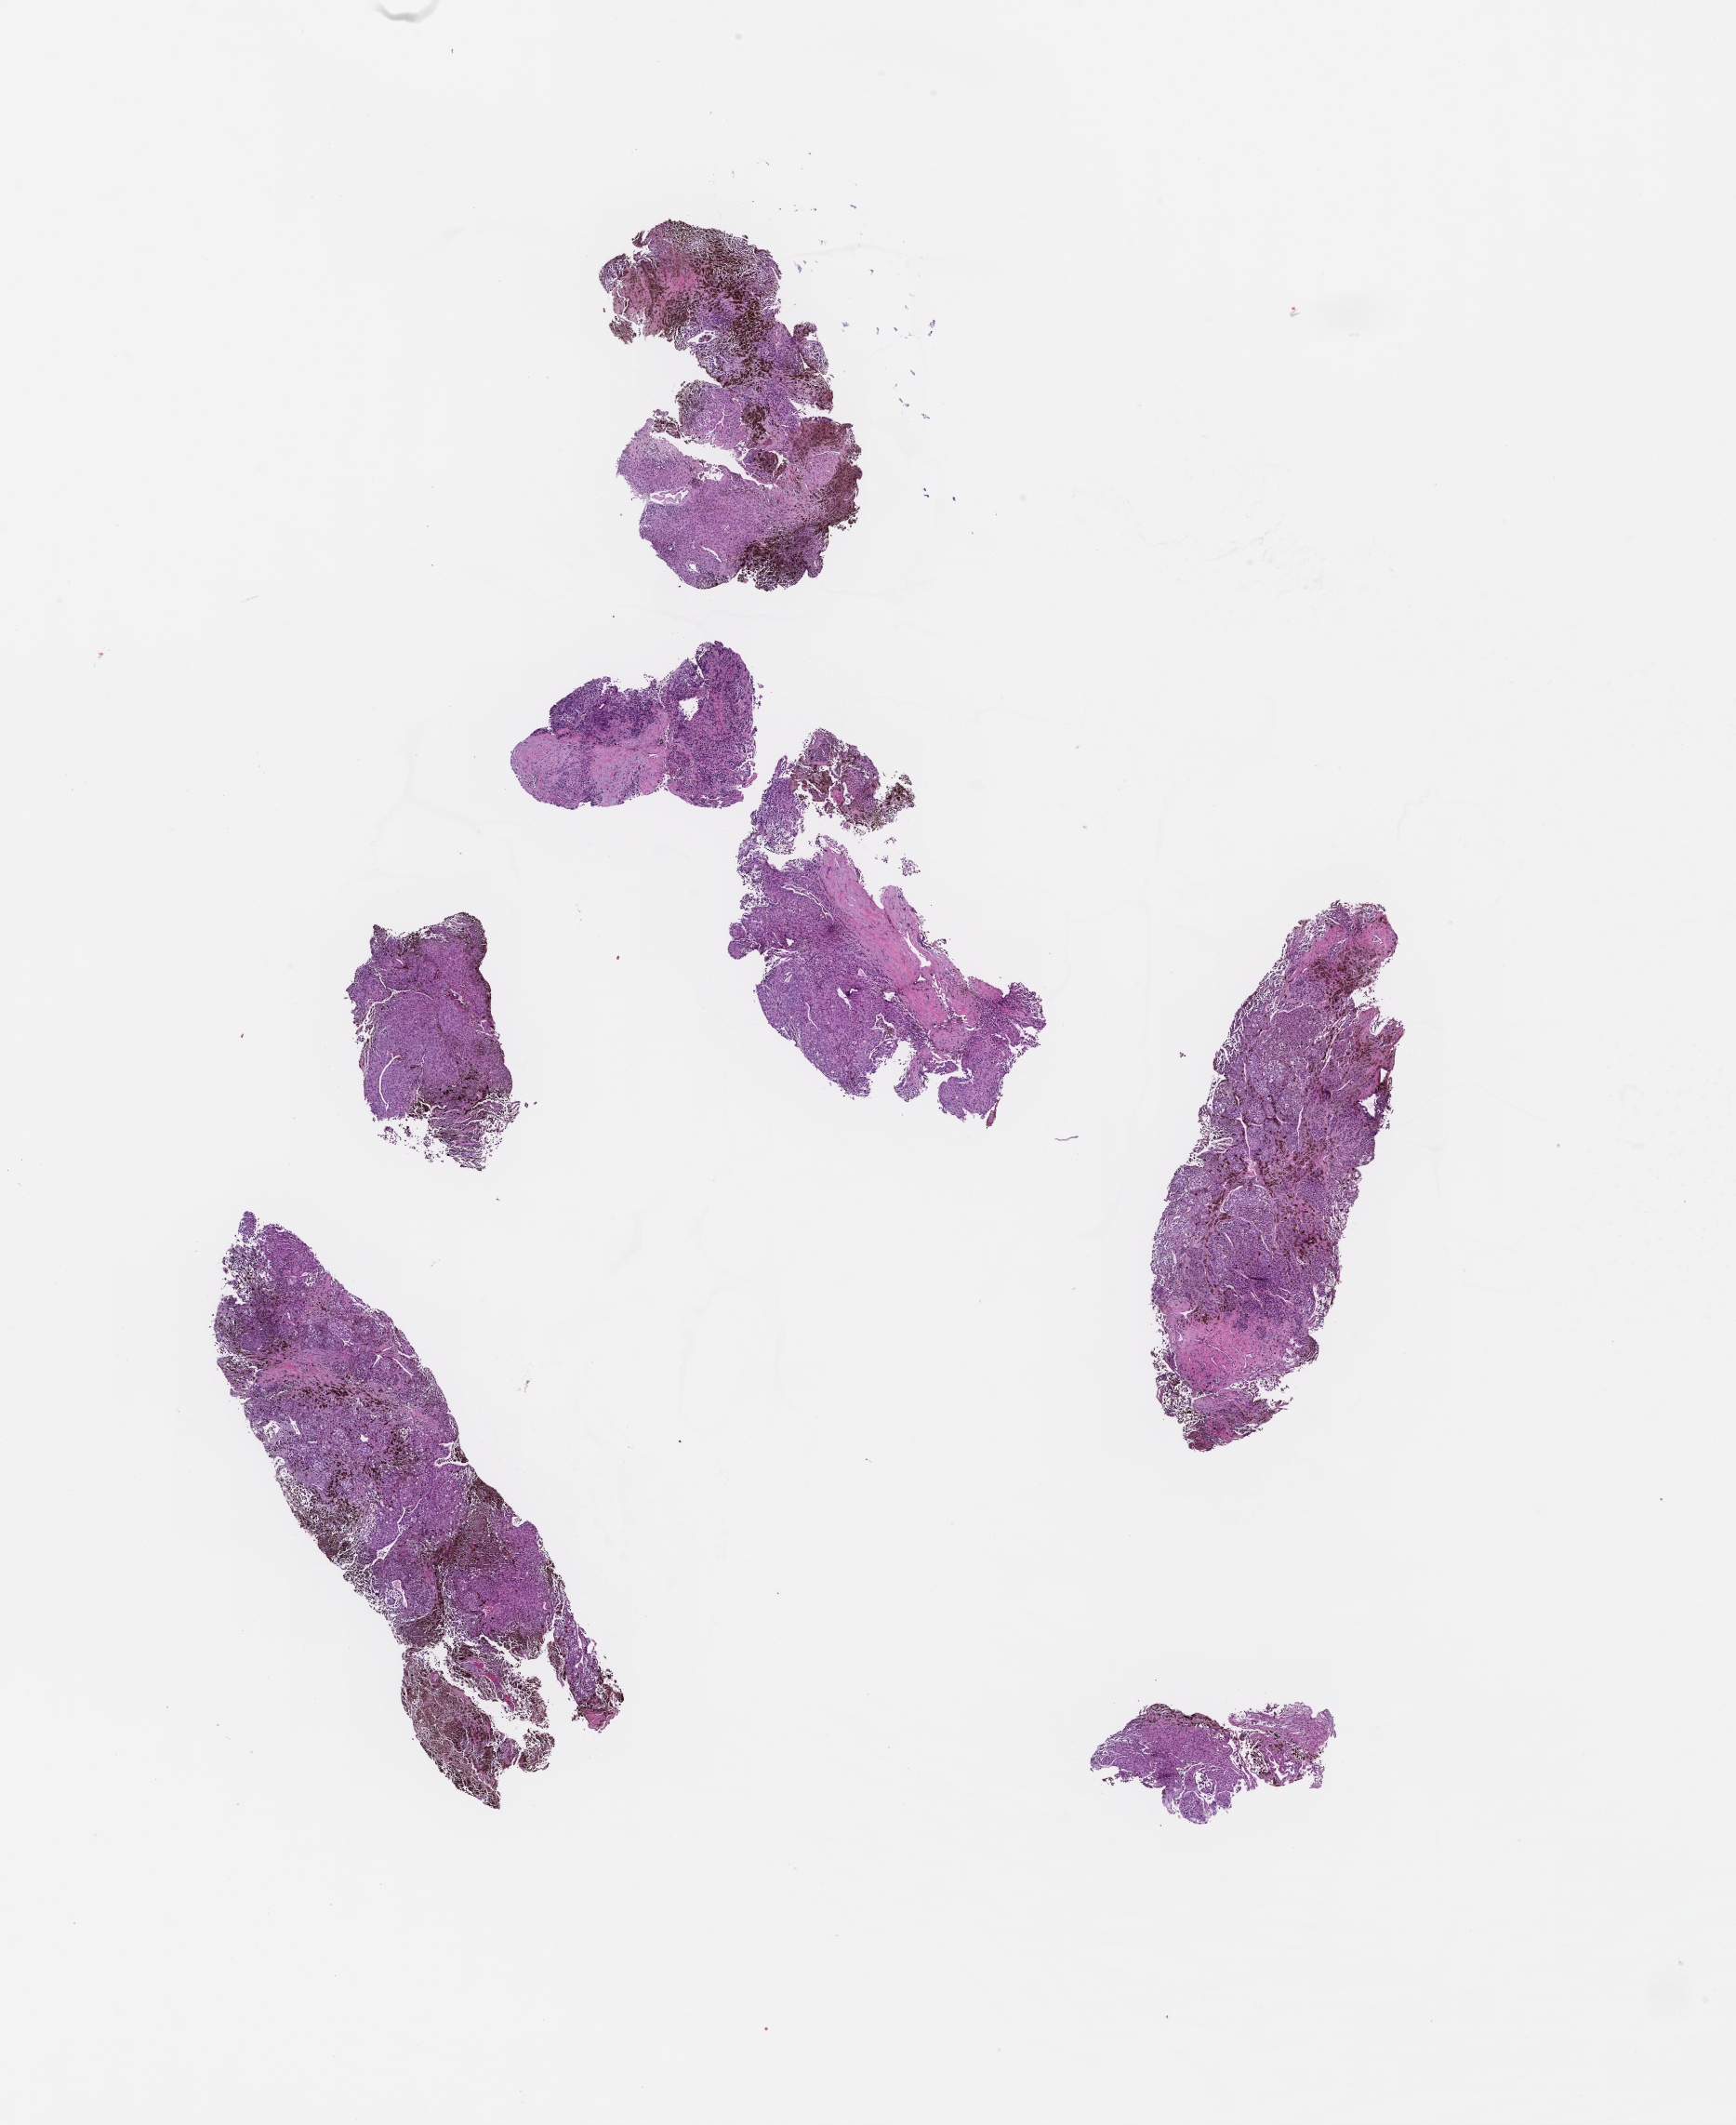
Digitized haematoxylin and eosin-stained section — a low-resolution overview of the entire scanned area, about 15.1 x 18.5 mm. Formalin-fixed paraffin-embedded section. Collected at baseline (before treatment). Female patient.
This section: metastasis (sampled organ not recorded). Patient diagnosis (primary): Melanoma.